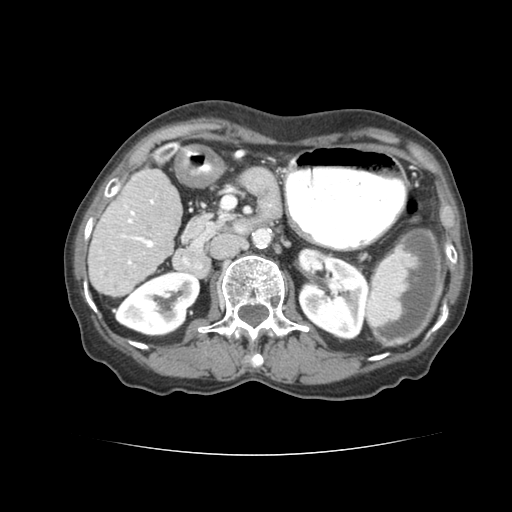
Contrast-enhanced abdominal CT (liver protocol), one axial slice; slice 26 of 77 in the series (ordered by position); reconstruction kernel STANDARD; soft-tissue window (W 400 / L 40 HU); 2.5 mm slice thickness; 512 × 512 image matrix, field of view 340 × 340 mm. From the clinical record (not read from this slice): diagnosis: hepatocellular carcinoma (patient treated with transarterial chemoembolisation; whether this scan precedes or follows treatment is not stated here); TNM stage (as recorded): Stage-I; Child-Pugh class: A; tumour differentiation: well differentiated; tumour nodularity: uninodular.
Outlined on this slice (semi-automatically segmented with operator editing):
- liver parenchyma outside the tumour (the mass and vessels are separate outlines, so this box may not span the whole liver): box from (x=86, y=168) to (x=180, y=294) px
- liver vessels: (x=116, y=189)–(x=153, y=264)